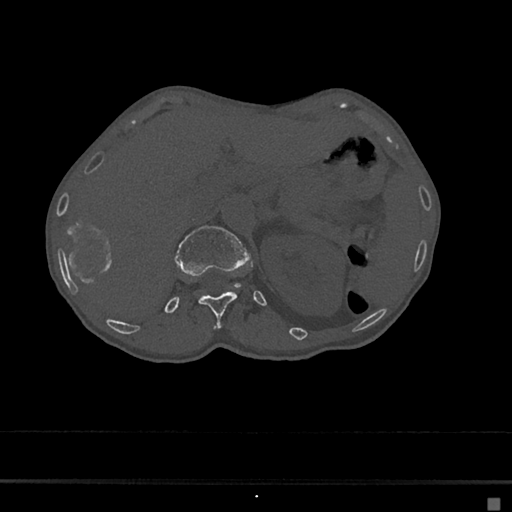
CT including the spine, one axial slice; position 107 of 797 along the scan axis; reconstruction kernel Br40s/3; 120 kVp; bone window (W 1800 / L 400 HU); 0.5 mm slice thickness; 512 × 512 image matrix, field of view 360 × 360 mm. Female patient, age 68 years. Case-level facts recorded for this patient, not image findings: primary cancer: renal.
Structures marked on this image (semi-automatically segmented with operator editing):
- L1 vertebra: bounding box (x1, y1, x2, y2) in pixels: (174, 226, 248, 275)
- T12 vertebra: (198, 291, 237, 327)